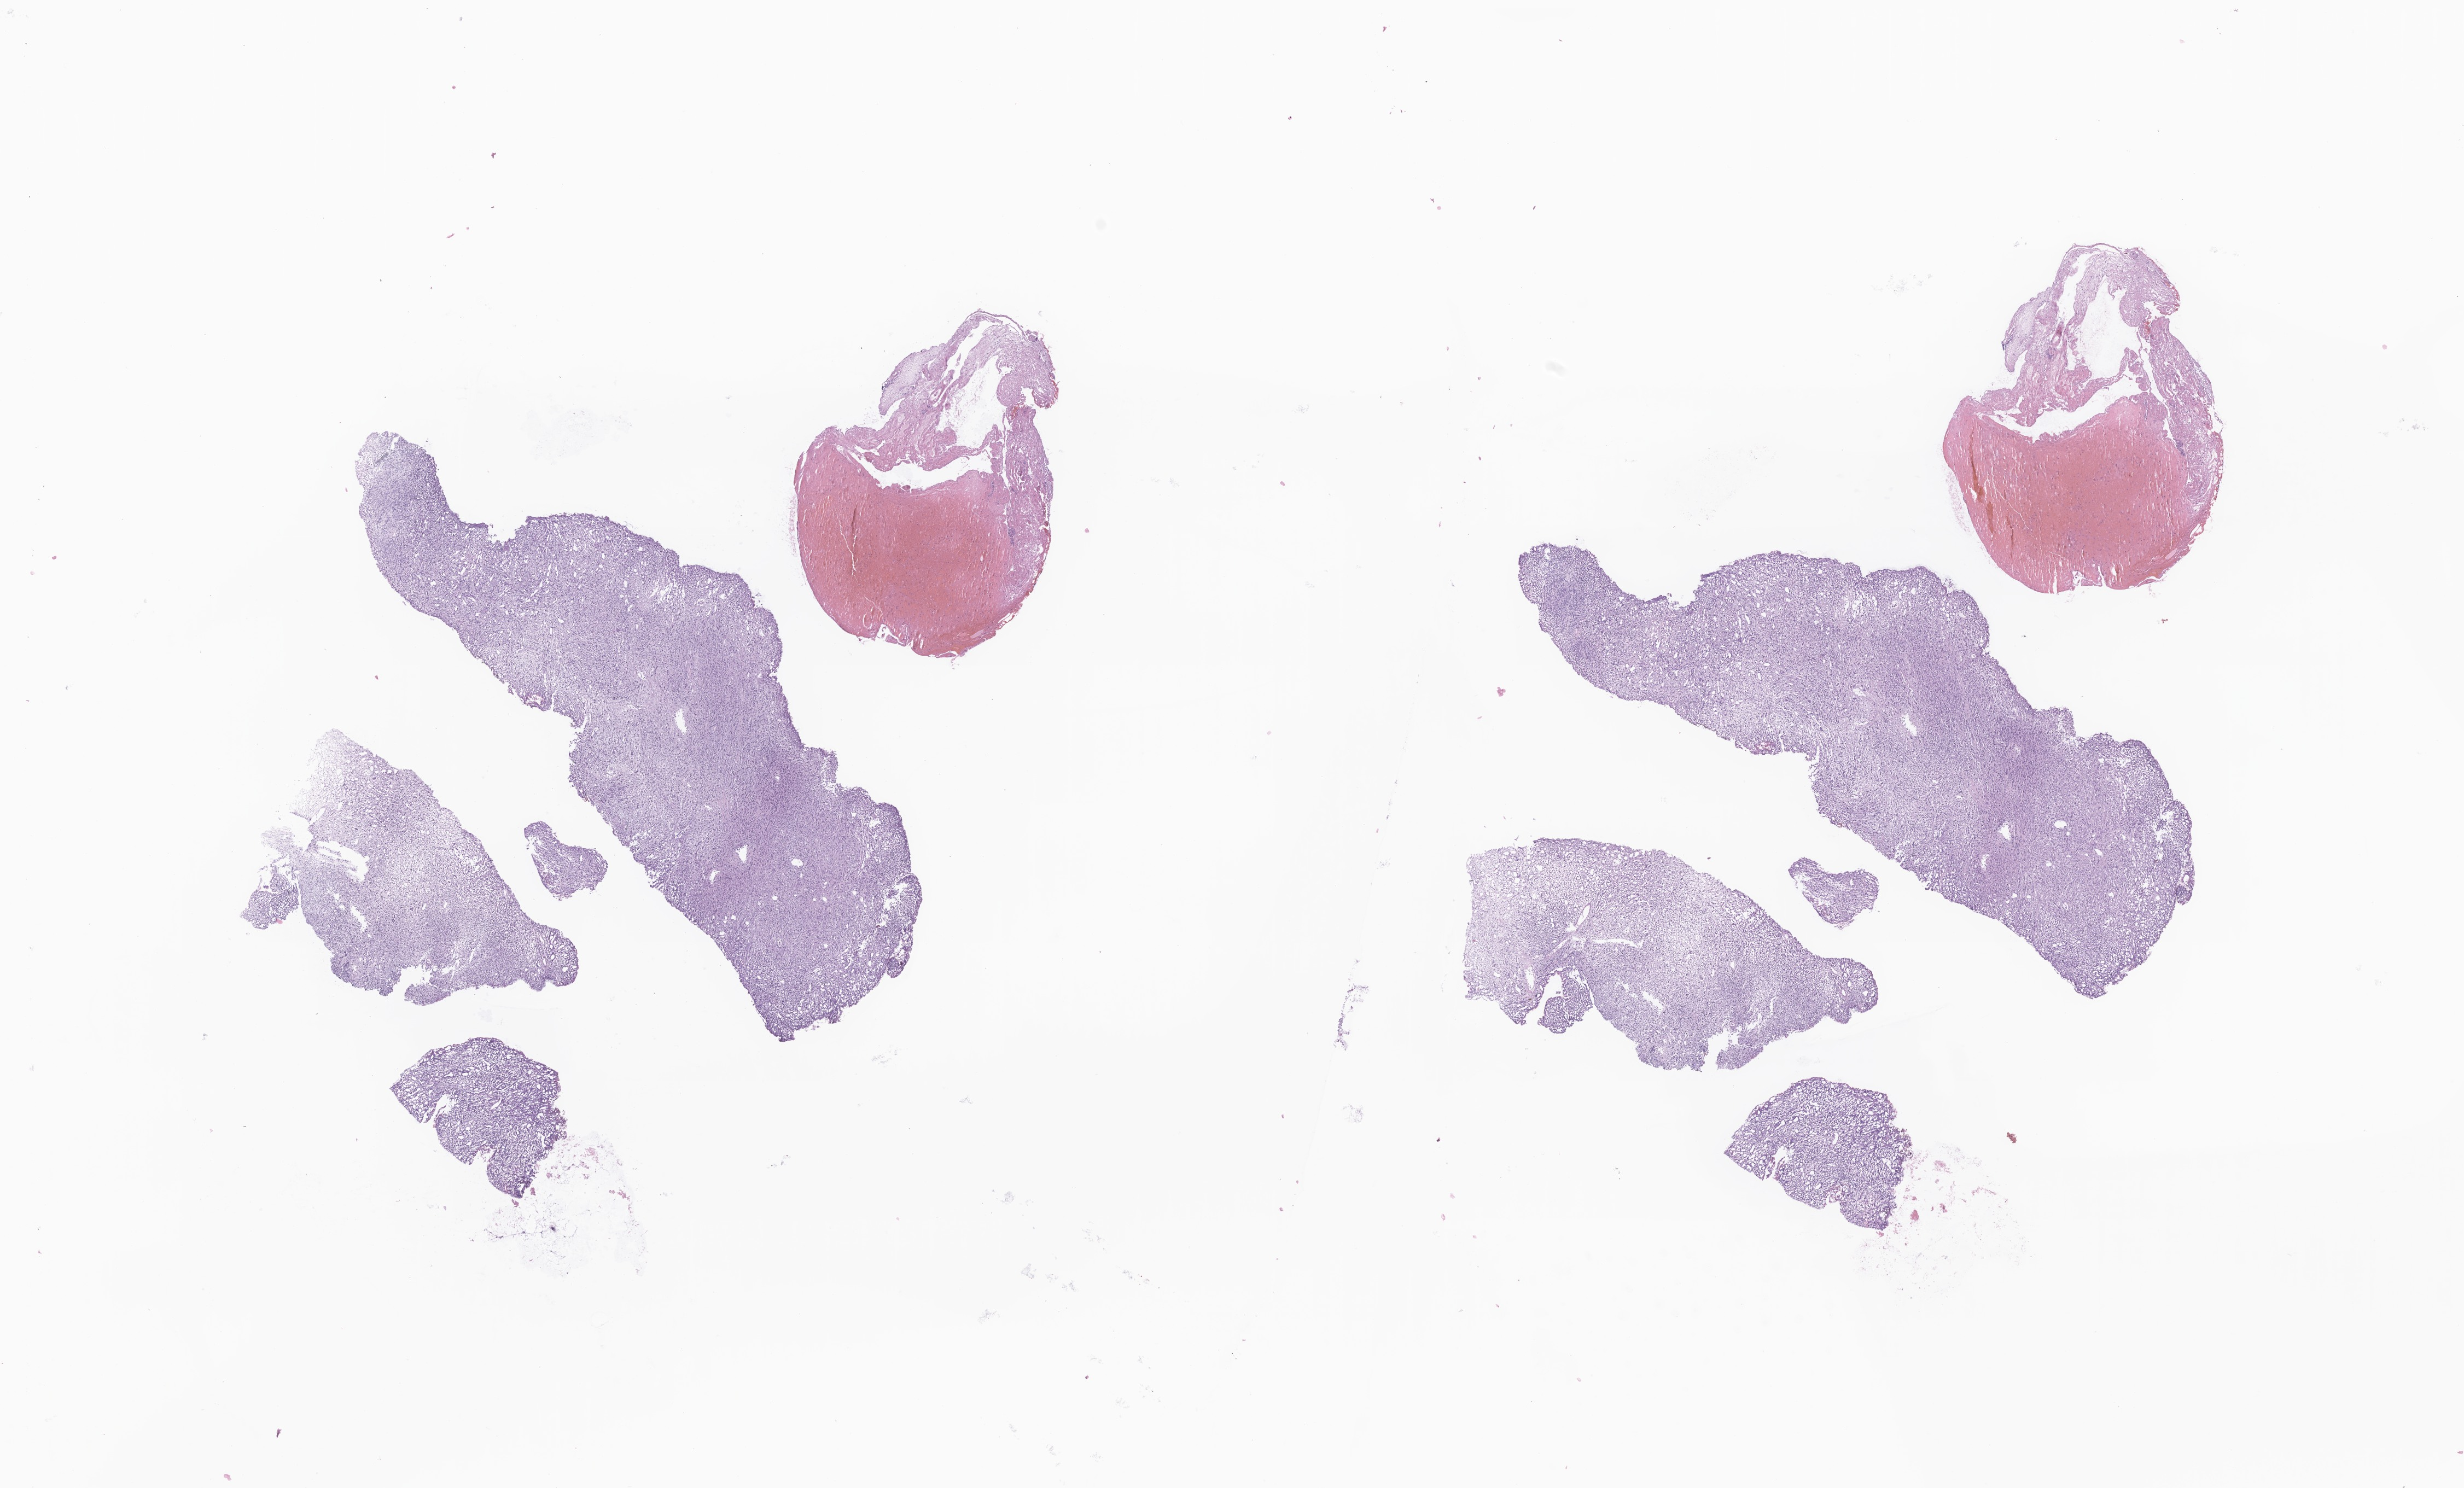
Whole-slide image, hematoxylin and eosin (H&E) stain of tumor tissue from the retroperitoneum, shown as a low-resolution overview of the whole scanned area (about 19.0 x 11.5 mm), formalin-fixed, paraffin-embedded (FFPE) tissue. Male patient, age 316 days.
Diagnosis: Rhabdomyosarcoma, NOS.